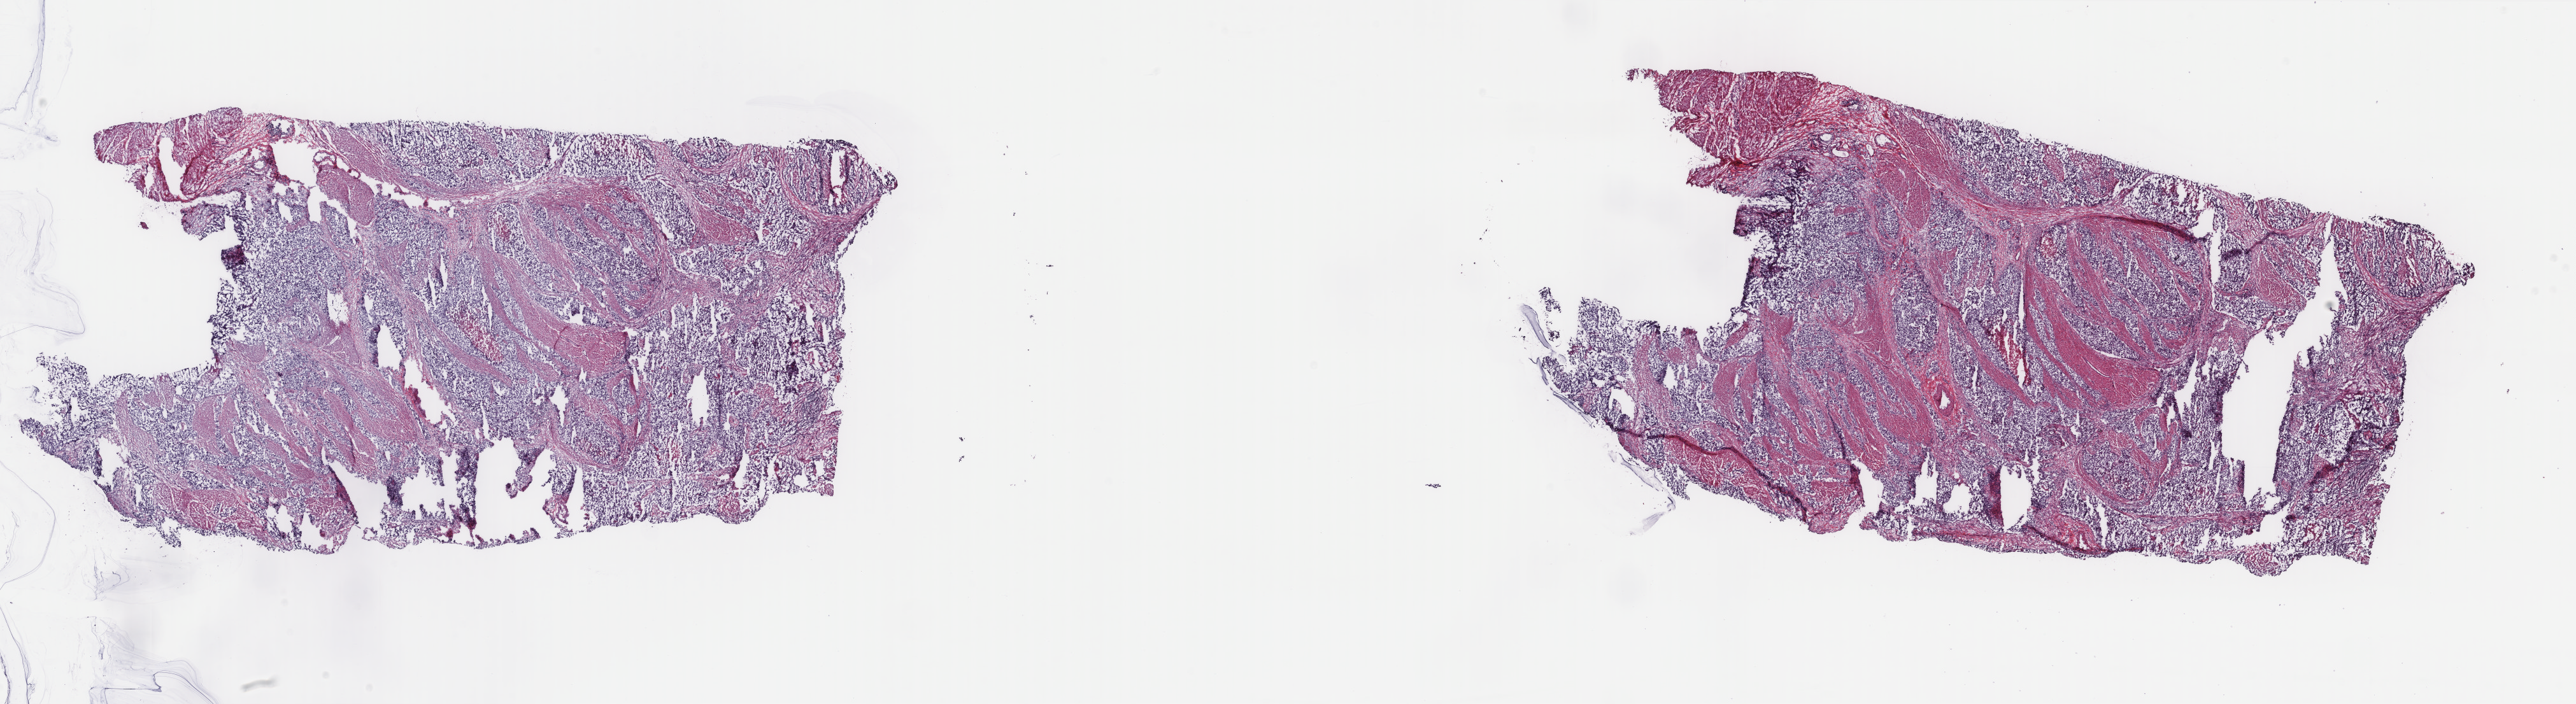
Whole-slide histology image, H&E-stained, shown as a low-resolution overview of the whole scanned area (about 32.1 x 8.8 mm). Frozen section from the top of the tissue portion. Sample: primary tumour, bladder. Patient: male, age at initial diagnosis 59 years.
Diagnosis: Transitional cell carcinoma (lateral wall of bladder).